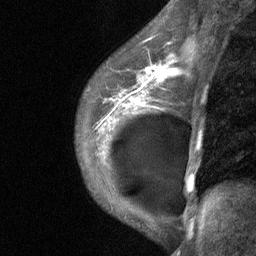
Breast MRI (dynamic contrast-enhanced), one sagittal slice. Slice 46 of 64 in the series (ordered by position). Dynamic contrast-enhanced study with each time point stored as its own series, time point 2 of 3 at this slice position (early post-contrast, ordered by acquisition time). 1.5 T. TE 4.8 ms, TR 27 ms. 2 mm slice thickness. 256 × 256 image matrix, field of view 180 × 180 mm. Female patient, age 35 years. From the clinical record (not read from this slice): setting: breast cancer imaged before/during neoadjuvant chemotherapy; receptor status: HR-positive, HER2-negative.
Structures marked on this image (semi-automatic segmentation, software-assisted and operator-edited):
- analysis volume of interest (the breast-tissue region the enhancement analysis was run in; not a lesion): bounding box (x1, y1, x2, y2) in pixels: (75, 58, 186, 171)
- tumour enhancement mask (voxels above the 90 % enhancement threshold inside the analysis volume of interest): (123, 65, 170, 102)